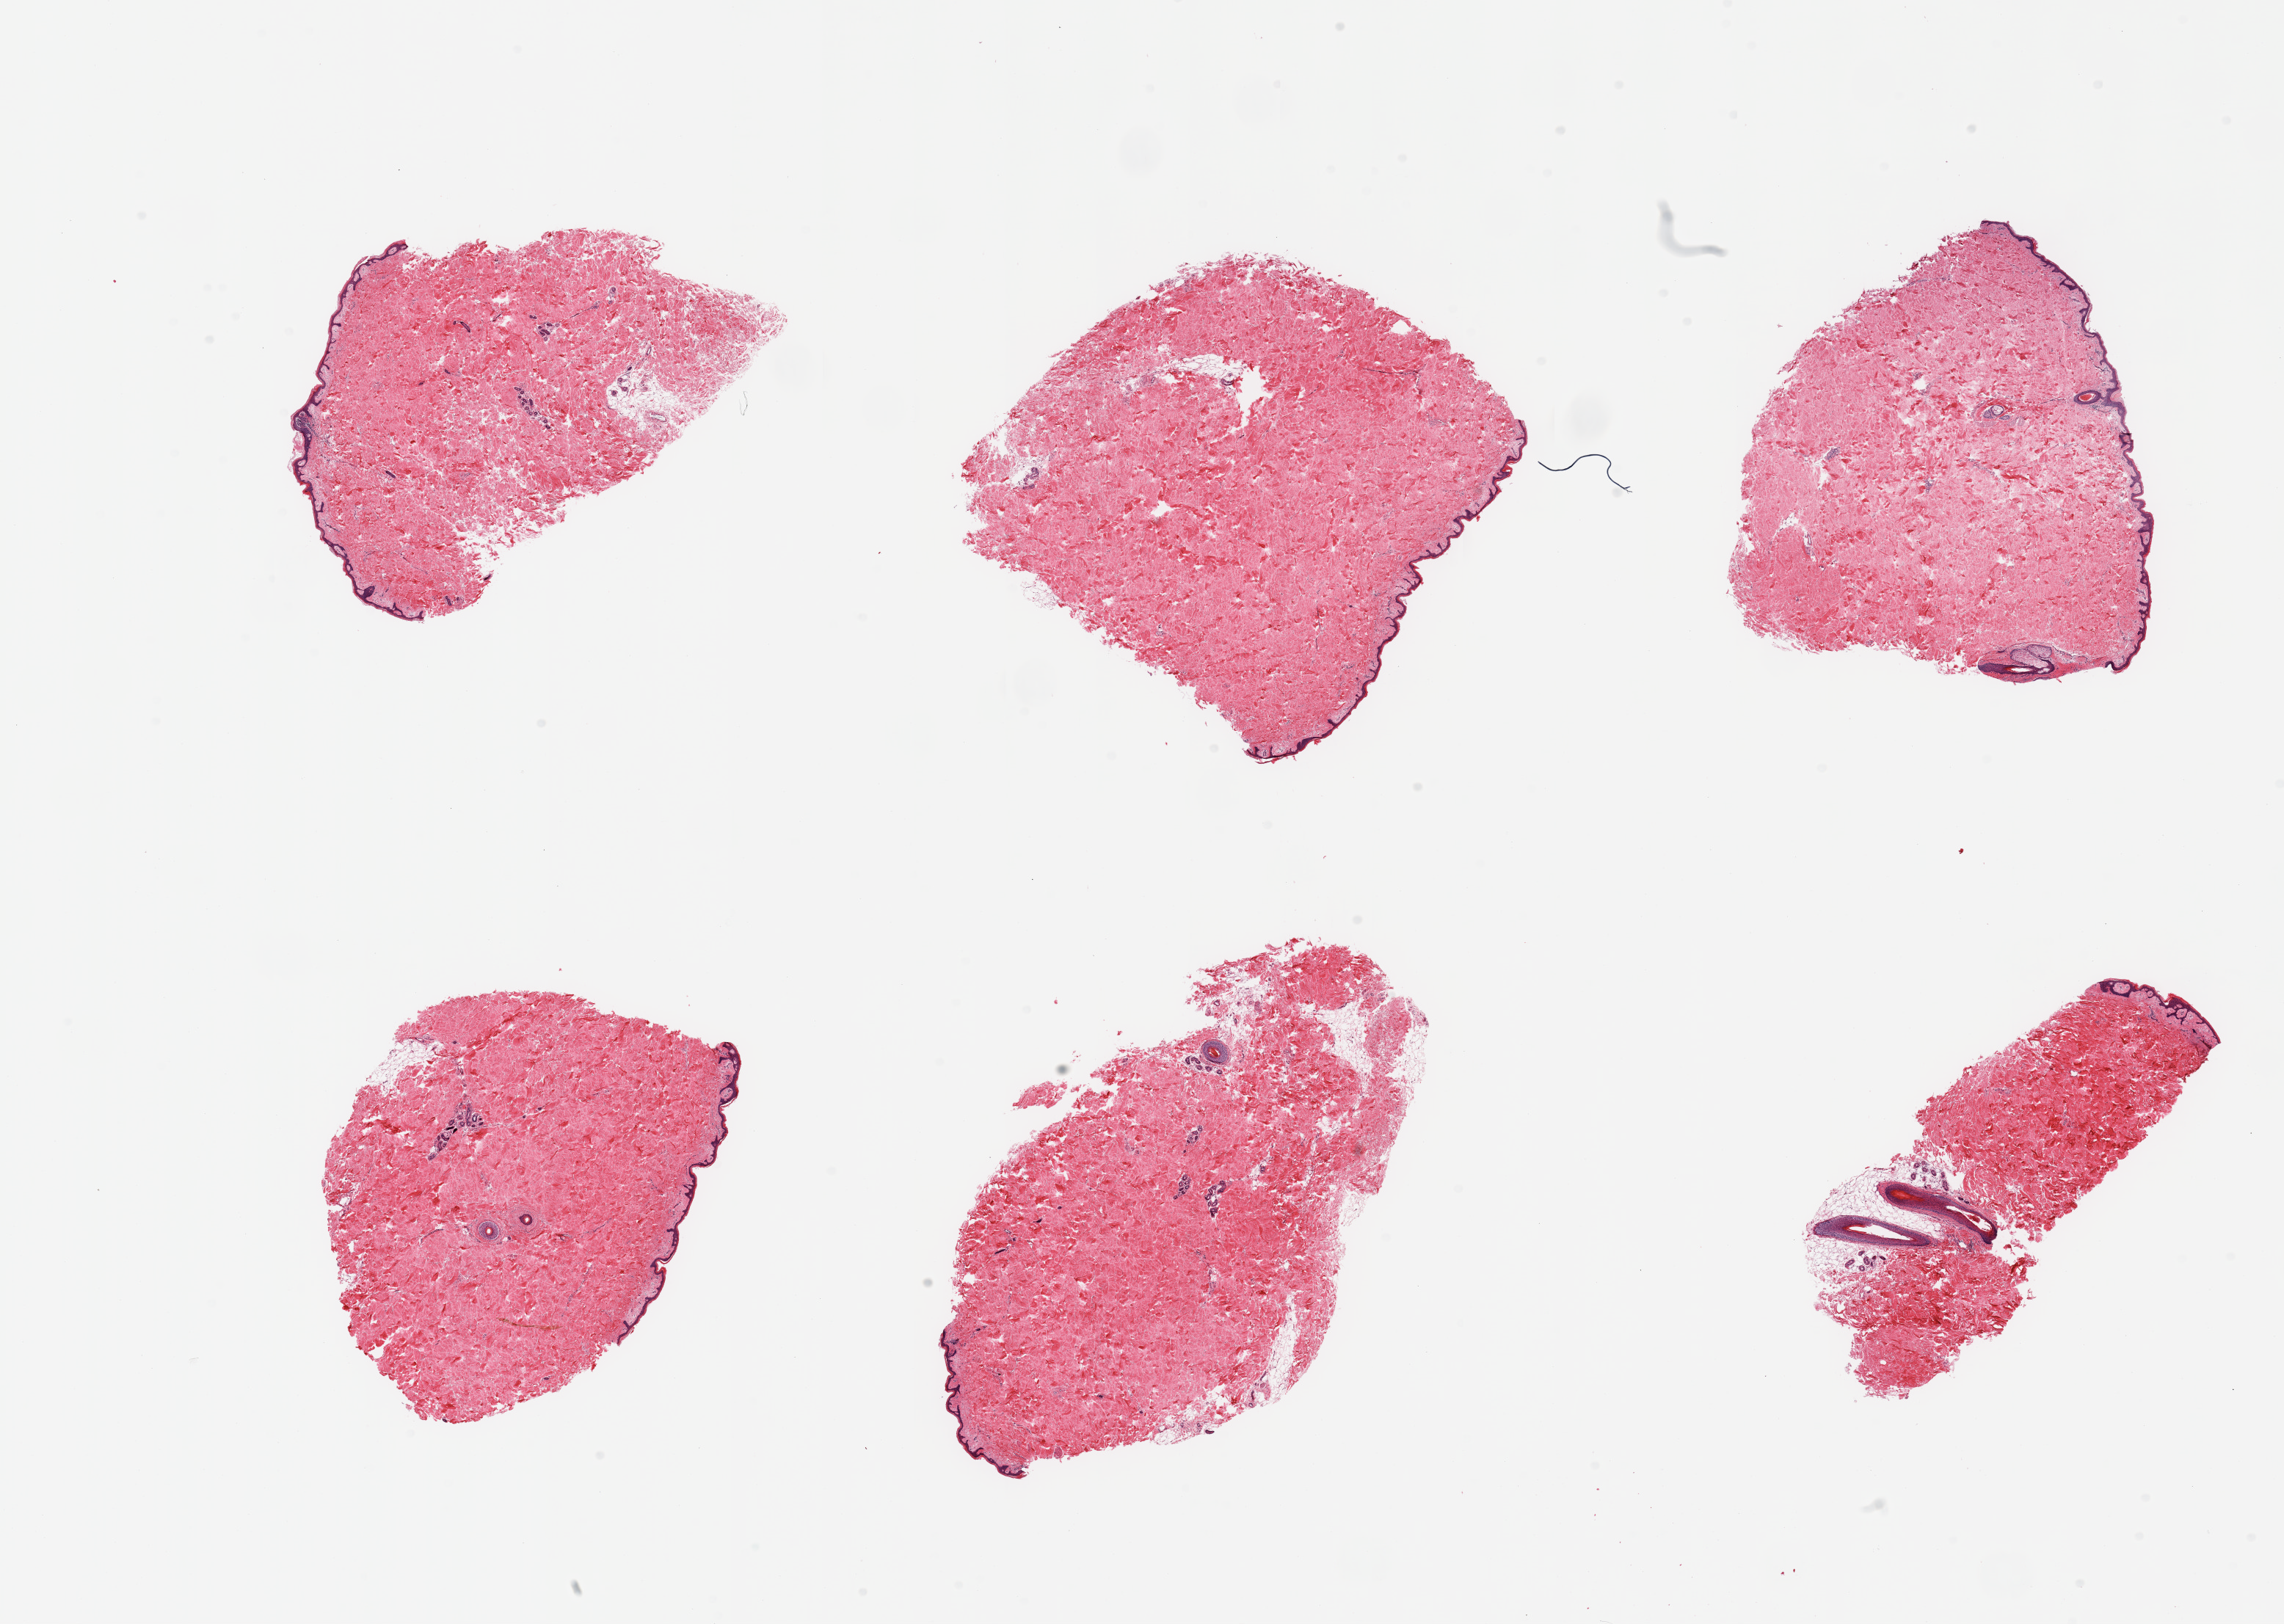
Whole-slide image, H&E stain, brightfield — a low-resolution overview of the entire scanned area, about 24.6 x 17.5 mm (slide scanned at 20x), PAXgene-fixed, paraffin-embedded tissue, sampled site (target tissue): skin of suprapubic region, tissue donor sample. Male donor.
Pathologist's review note for this sample: 6 pieces, no dermal fat; squamous epithelium is ~30 microns.